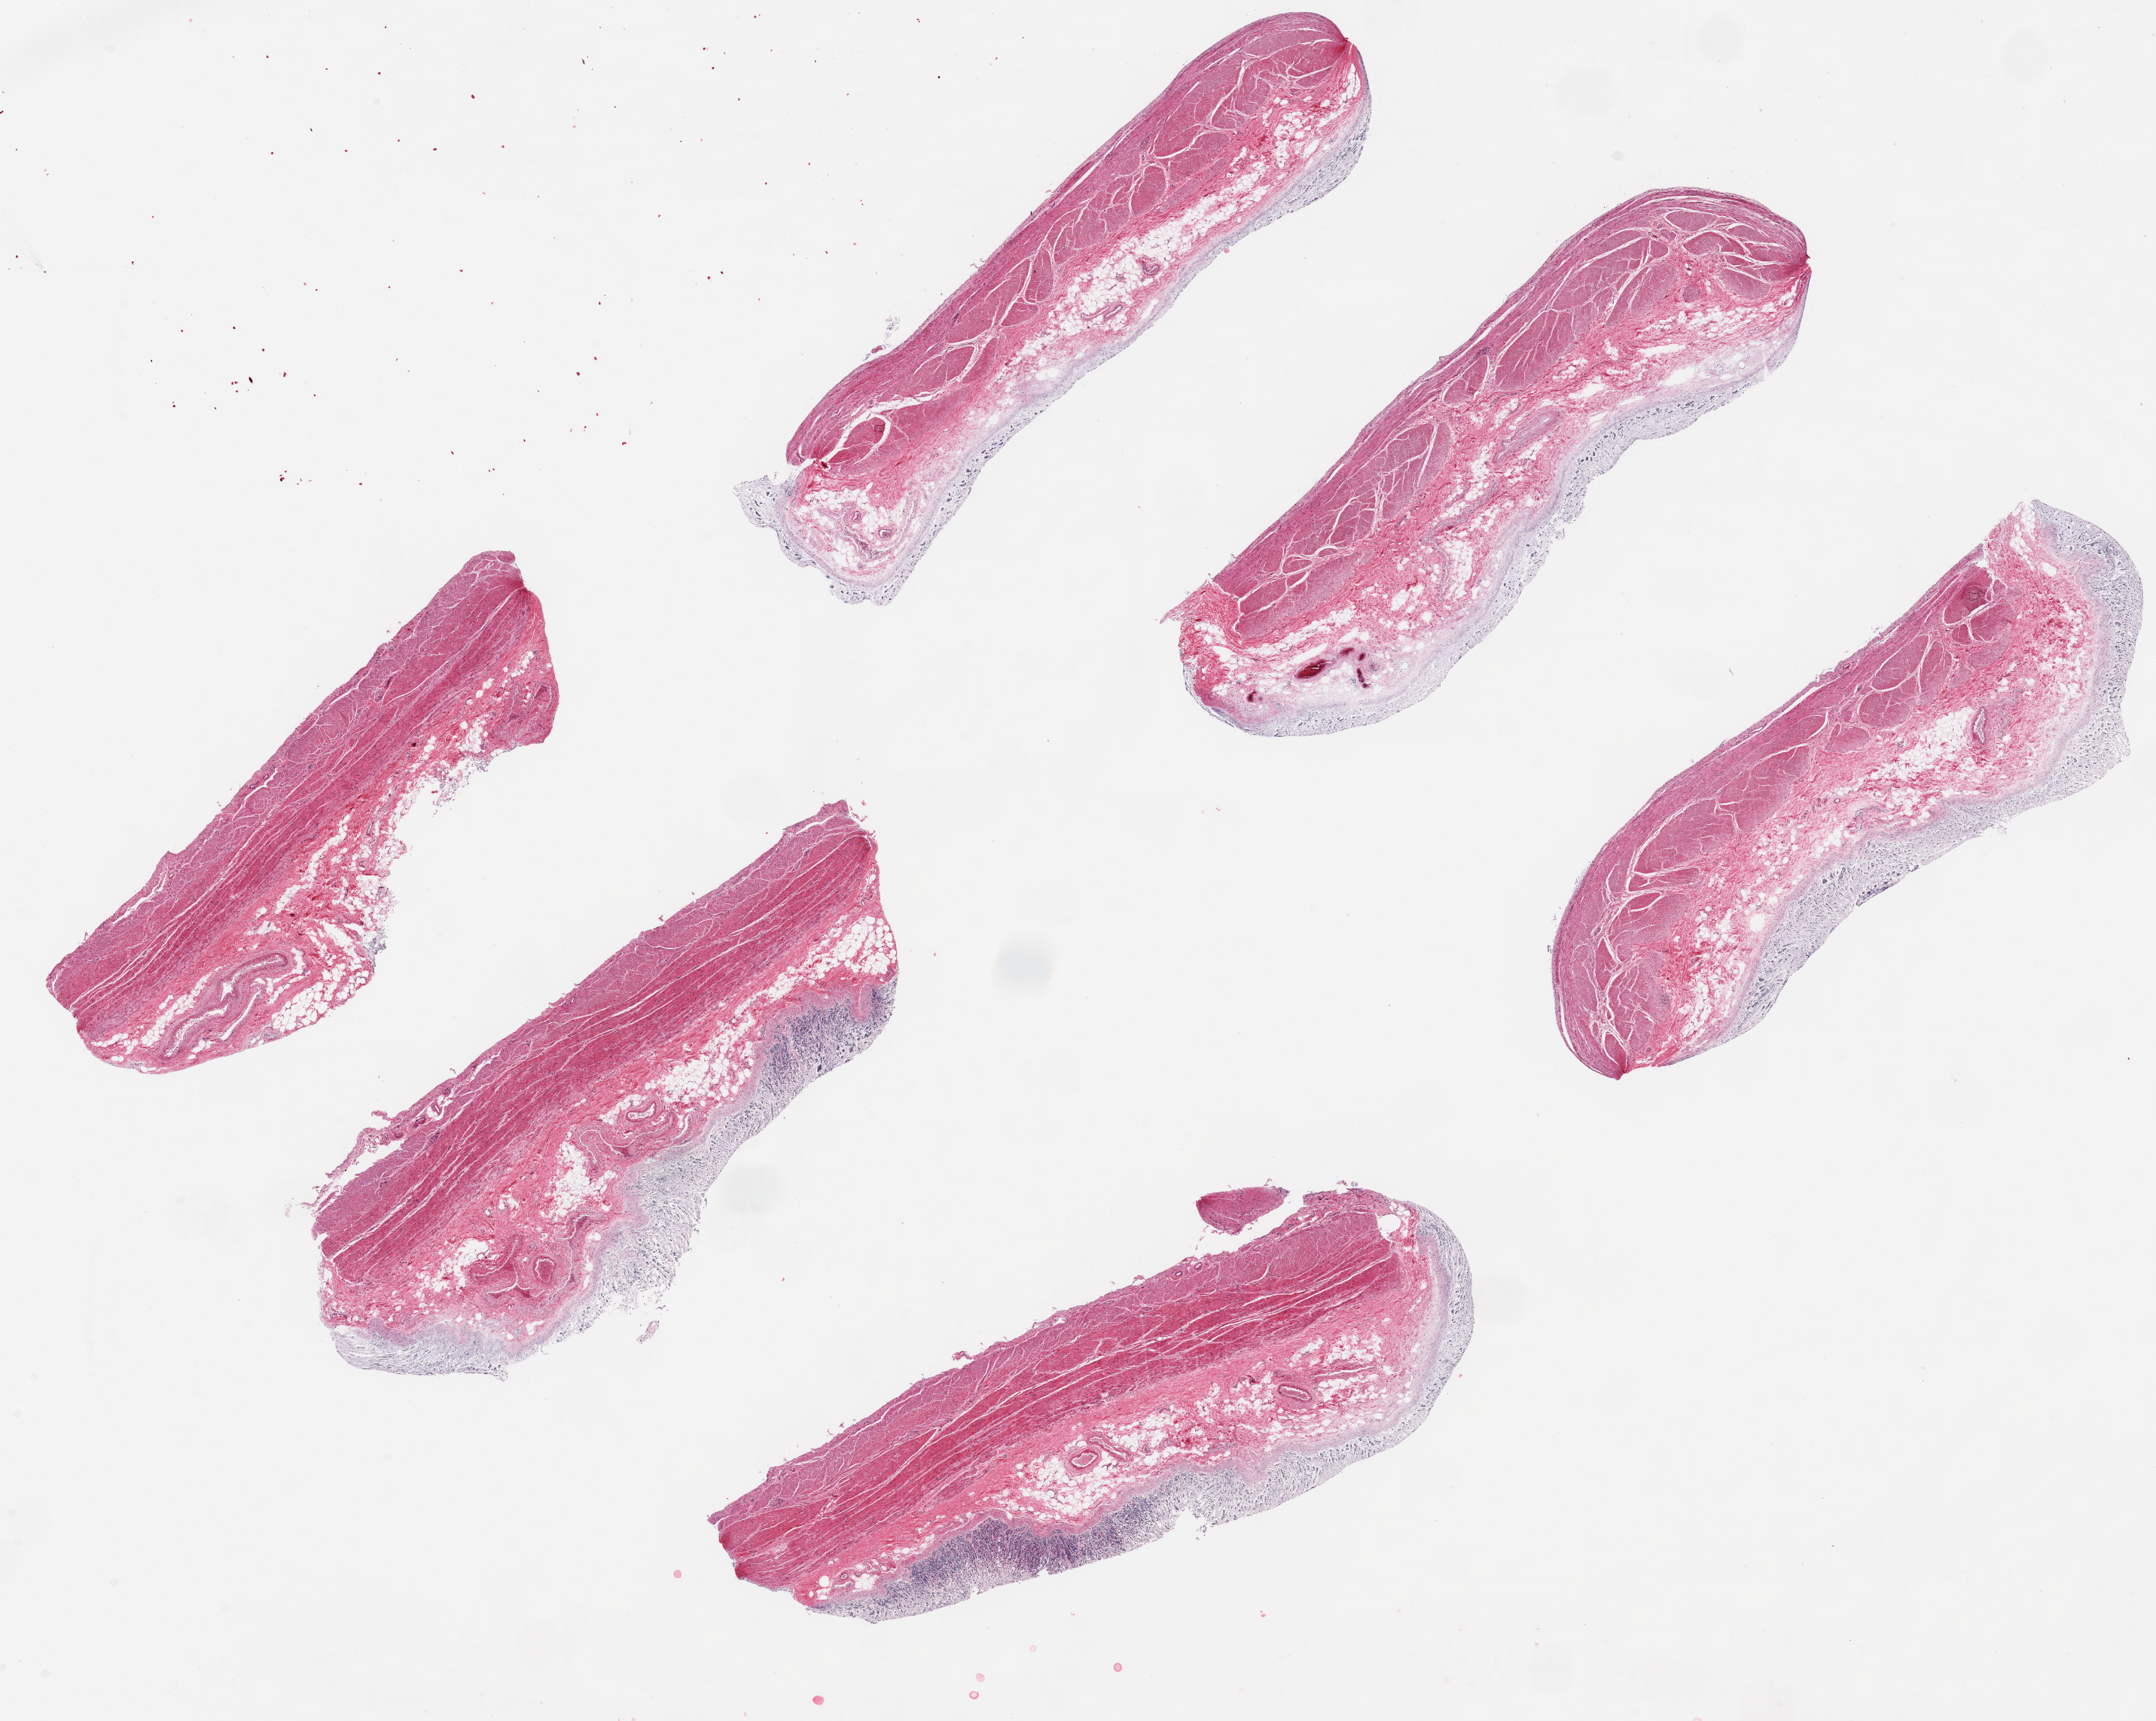
Whole-slide image, hematoxylin and eosin (H&E) stain, brightfield — shown as a low-resolution overview of the whole scanned area (about 22.6 x 18.1 mm, slide scanned at 20x); PAXgene-fixed, paraffin-embedded tissue; target tissue: stomach; donor tissue sample. Donor sex: male.
• reviewer comment on this tissue sample: 6 ~ 8x2.5mm pieces, epithelial component of mucosa completely autolyzed